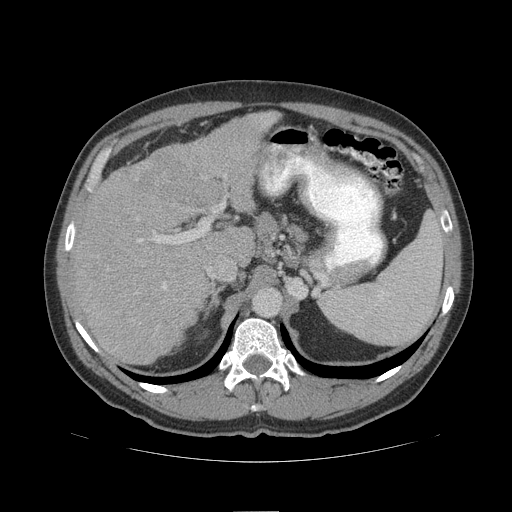
Contrast-enhanced abdominal CT (liver protocol), one axial slice. Position 68 of 109 along the scan axis. Reconstruction kernel STANDARD. Soft-tissue window (W 400 / L 40 HU). 2.5 mm slice thickness. 512 × 512 image matrix. From the clinical record (not read from this slice): diagnosis: hepatocellular carcinoma (patient treated with transarterial chemoembolisation; whether this scan precedes or follows treatment is not stated here); TNM stage (as recorded): Stage-IIIB; Child-Pugh class: A; tumour differentiation: poorly differentiated.
Structures marked on this image (semi-automatically segmented with operator editing):
- liver parenchyma outside the tumour (the mass and vessels are separate outlines, so this box may not span the whole liver): bounding box [x1, y1, x2, y2] px = [72, 110, 280, 364]
- mass: [138, 148, 227, 209]
- liver vessels: [138, 203, 225, 289]